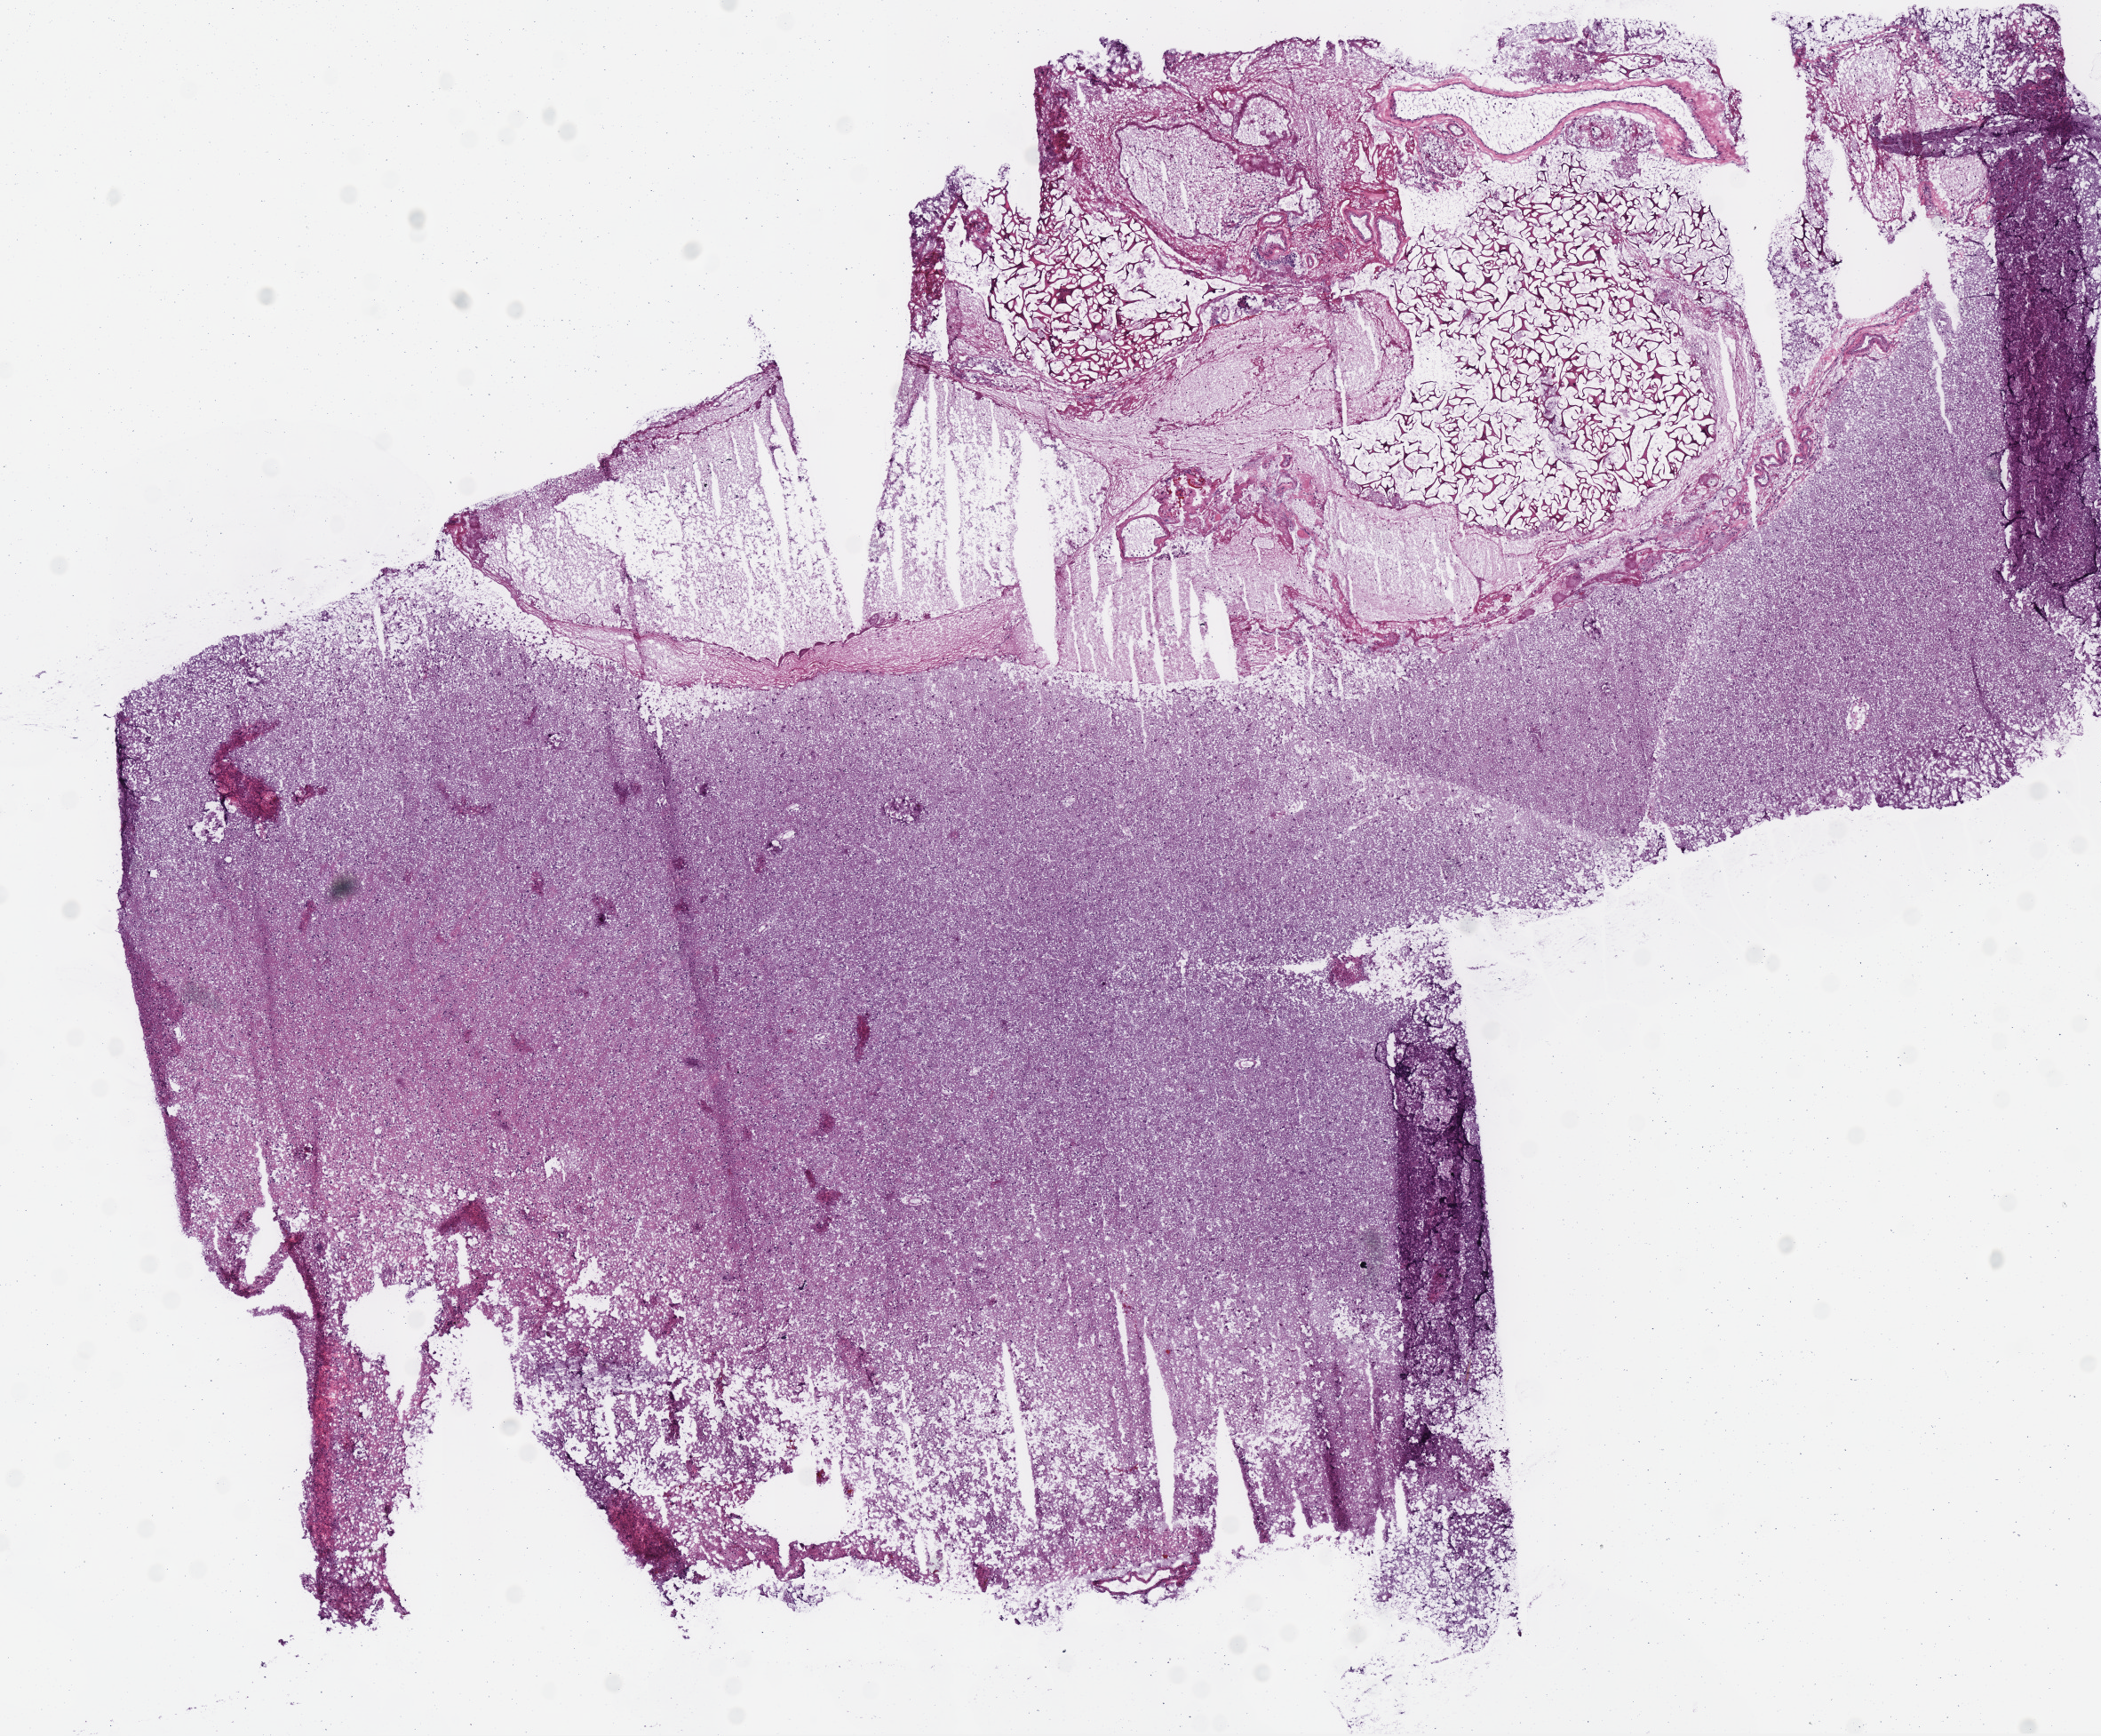
Hematoxylin and eosin (H&E) stained whole-slide image — shown as a low-resolution overview of the whole scanned area (about 9.3 x 7.7 mm, acquisition: 40x scan), frozen section from the top of the tissue portion, sample: primary tumour, brain. Female patient; age at initial diagnosis 49 years. Histologic grade: G2 (moderately differentiated). Slide review estimates, as recorded: tumour cells 90%, tumour nuclei 60%, normal cells 0%, stromal cells 10%, necrosis 0%.
Pathologic diagnosis: Oligodendroglioma, NOS (cerebrum). Laterality: left.